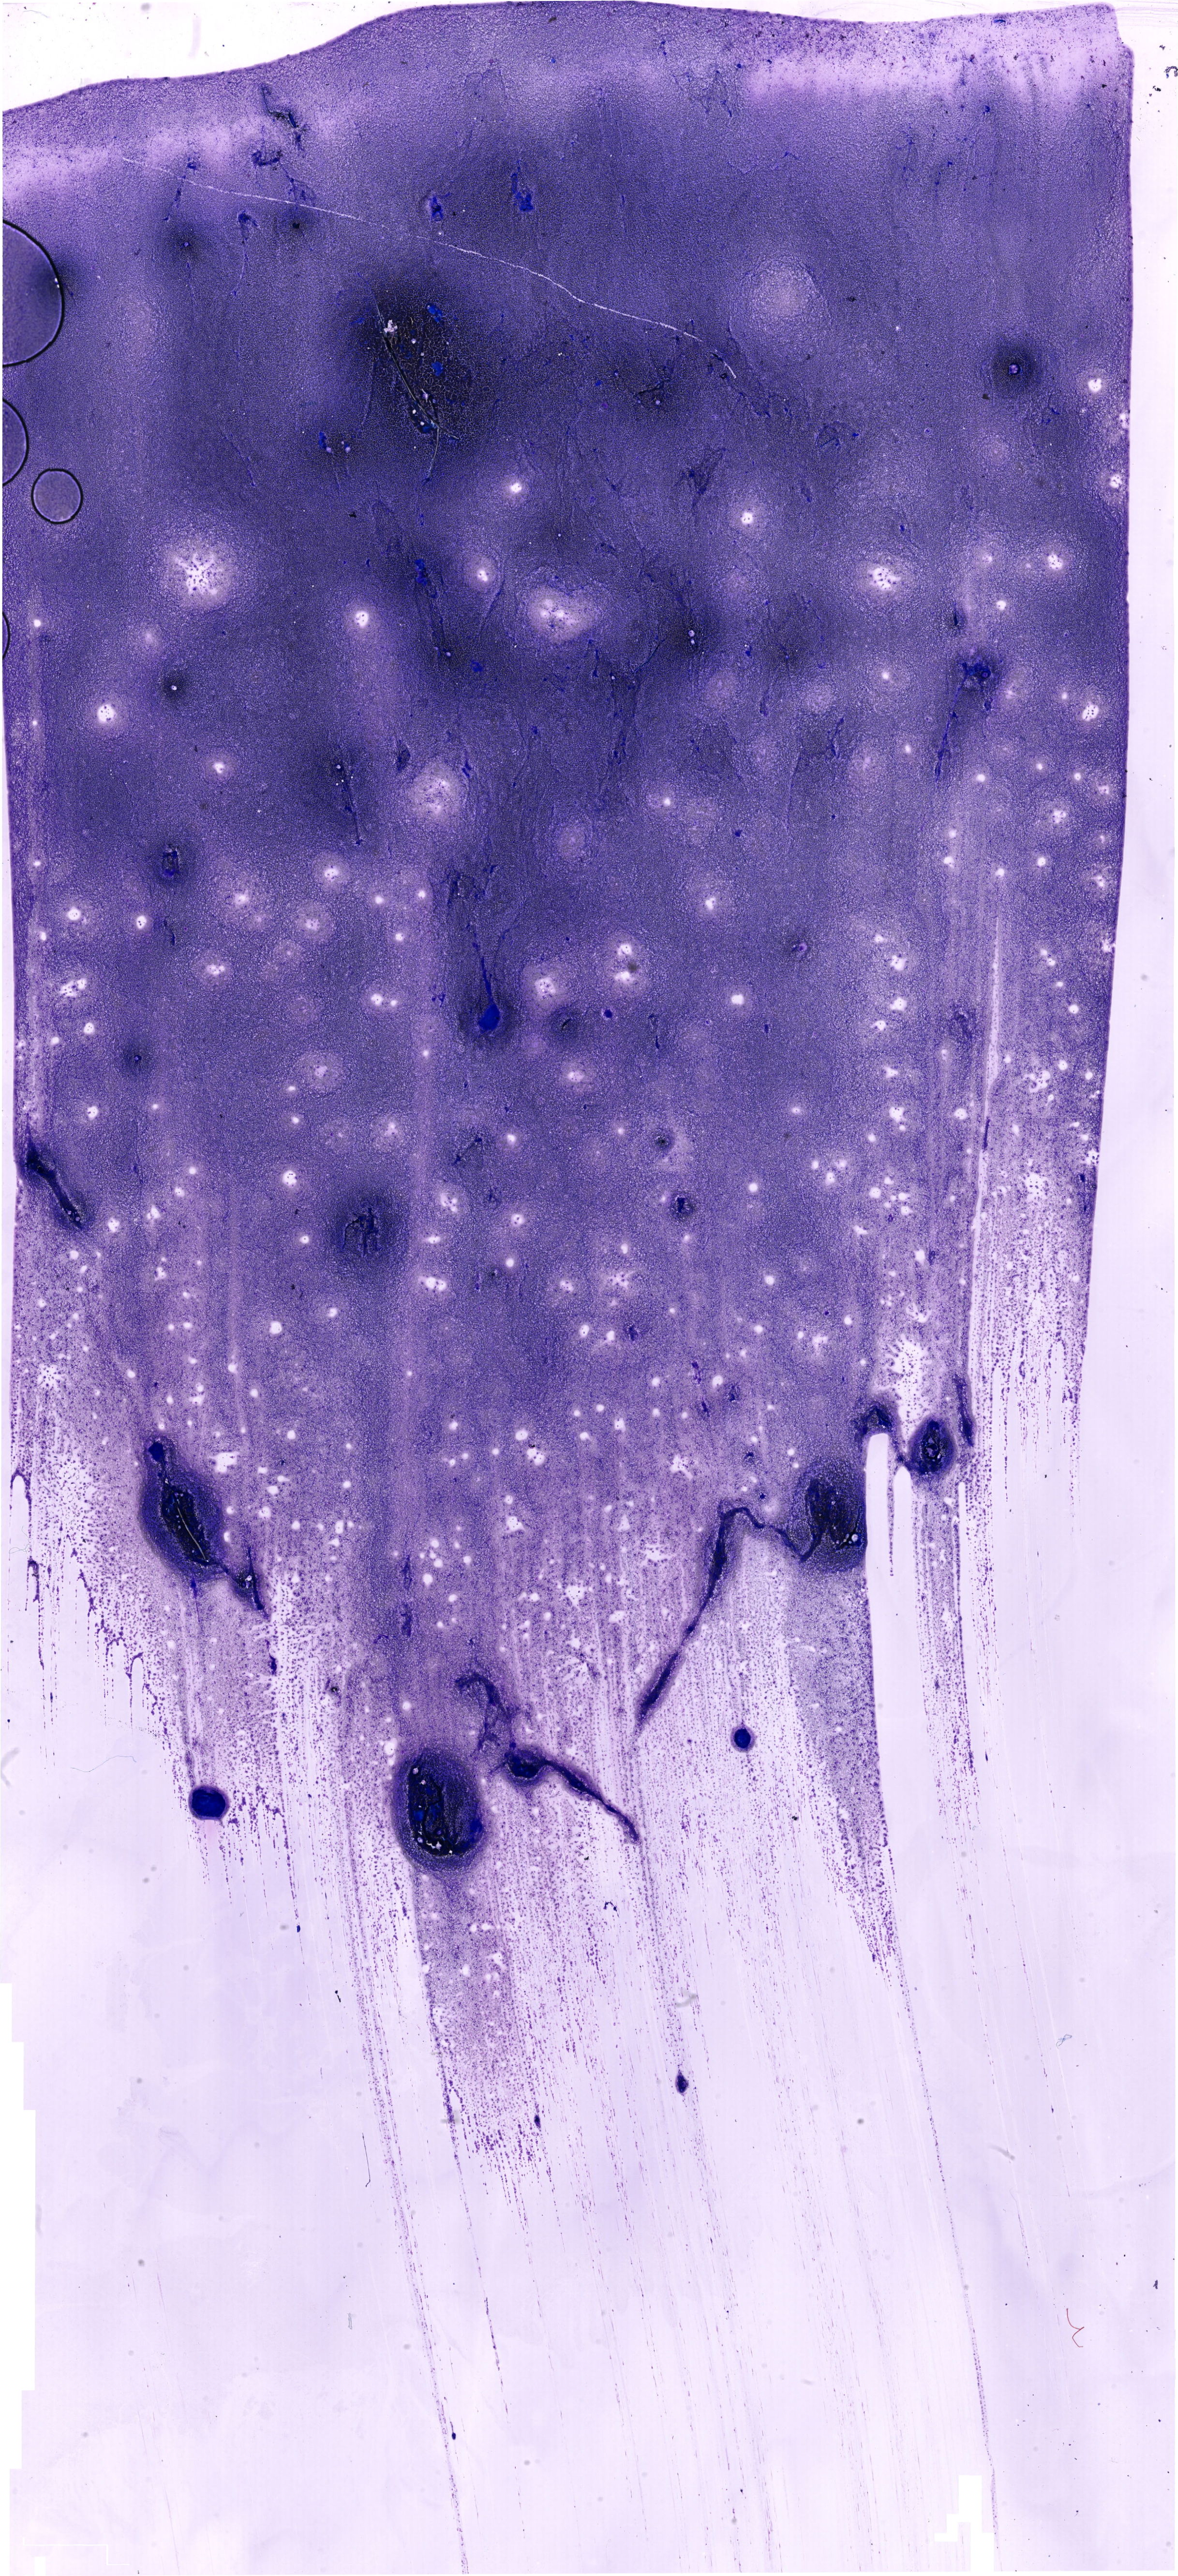
May-Grünwald-Giemsa (MGG)-stained marrow aspirate smear (whole slide) — low-resolution overview of the scanned area, about 19.0 x 41.6 mm. Patient sex: male.
Diagnosis: Blast Phase Chronic Myeloid Leukemia, BCR-ABL1 Positive.